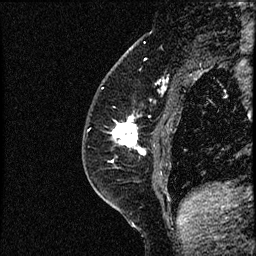
Breast MRI (dynamic contrast-enhanced), one sagittal slice; slice 21 of 52 in the series (ordered by position); dynamic contrast-enhanced study with each time point stored as its own series, time point 2 of 3 at this slice position (early post-contrast, ordered by acquisition time); 1.5 T; TE 4.2 ms, TR 17.6 ms; 256 × 256 image matrix, field of view 200 × 200 mm. Female patient, age 49 years. From the clinical record (not read from this slice): setting: breast cancer imaged before/during neoadjuvant chemotherapy; receptor status: HER2-positive.
Outlined on this slice (semi-automatically segmented with operator editing):
- analysis volume of interest (the breast-tissue region the enhancement analysis was run in; not a lesion): bounding box (x1, y1, x2, y2) in pixels: (85, 65, 182, 175)
- tumour enhancement mask (voxels above the 100 % enhancement threshold inside the analysis volume of interest): (114, 117, 146, 155)